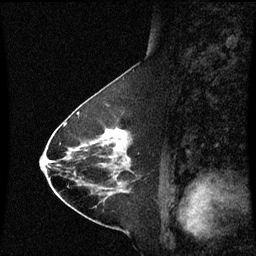
Breast MRI (dynamic contrast-enhanced), one sagittal slice; slice 30 of 60 in the series (ordered by position); dynamic contrast-enhanced series, image 2 of 3 at this slice position (ordered by acquisition); 1.5 T; TE 4.2 ms, TR 8.9 ms; 256 × 256 image matrix. Female patient, age 63 years. From the clinical record (not read from this slice): setting: breast cancer imaged before/during neoadjuvant chemotherapy; receptor status: HR-positive, HER2-negative.
Outlined on this slice (semi-automatically segmented with operator editing):
- analysis volume of interest (the breast-tissue region the enhancement analysis was run in; not a lesion): bounding box <94,128,133,177> (left, top, right, bottom; pixels)
- tumour enhancement mask (voxels above the 70 % enhancement threshold inside the analysis volume of interest): <106,130,130,161>